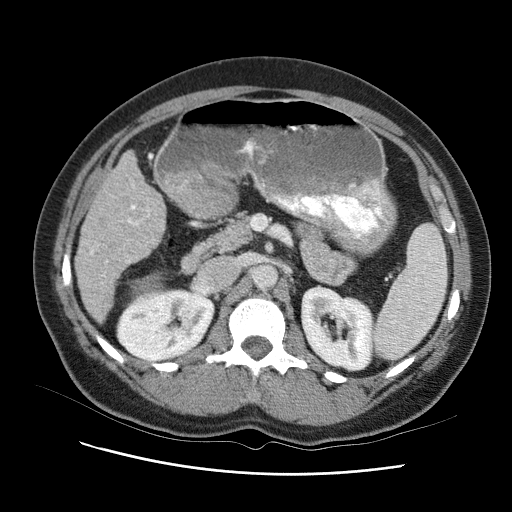
Contrast-enhanced abdominal CT (liver protocol), one axial slice; position 40 of 95 along the scan axis; reconstruction kernel STANDARD; one of 2 acquisitions stored at this slice position; soft-tissue window (W 400 / L 40 HU); 2.5 mm slice thickness; 512 × 512 image matrix, field of view 360 × 360 mm. Case-level facts recorded for this patient, not image findings: diagnosis: hepatocellular carcinoma (patient treated with transarterial chemoembolisation; whether this scan precedes or follows treatment is not stated here); TNM stage (as recorded): Stage-I; Child-Pugh class: B; tumour differentiation: moderately differentiated.
Annotated regions visible in this slice (semi-automatically segmented with operator editing):
- liver parenchyma outside the tumour (the mass and vessels are separate outlines, so this box may not span the whole liver): bounding box (x1, y1, x2, y2) in pixels: (74, 138, 172, 330)
- mass: (108, 253, 178, 304)
- liver vessels: (95, 173, 148, 325)